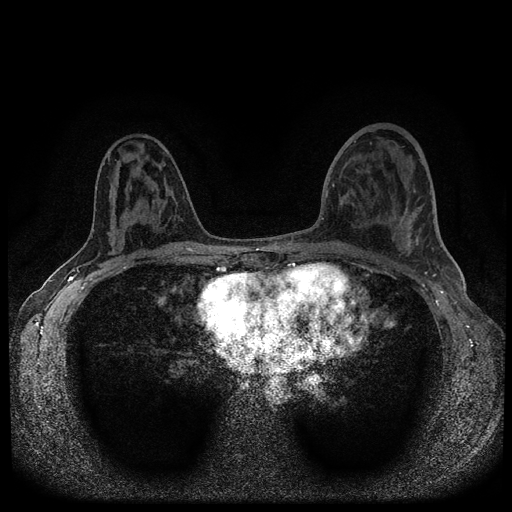
Breast MRI (dynamic contrast-enhanced, multi-phase), one axial slice; position 57 of 116 along the scan axis; dynamic contrast-enhanced series, time point 2 of 5 at this slice position (early post-contrast); 1.5 T; TE 2.7 ms, TR 5.6 ms; 2 mm slice thickness; 512 × 512 image matrix, field of view 310 × 310 mm. Patient: female, 40 years.
Structures marked on this image (semi-automatic segmentation, software-assisted and operator-edited):
- breast lesion (labelled benign in the annotation): bounding box [x1, y1, x2, y2] px = [124, 204, 130, 218]